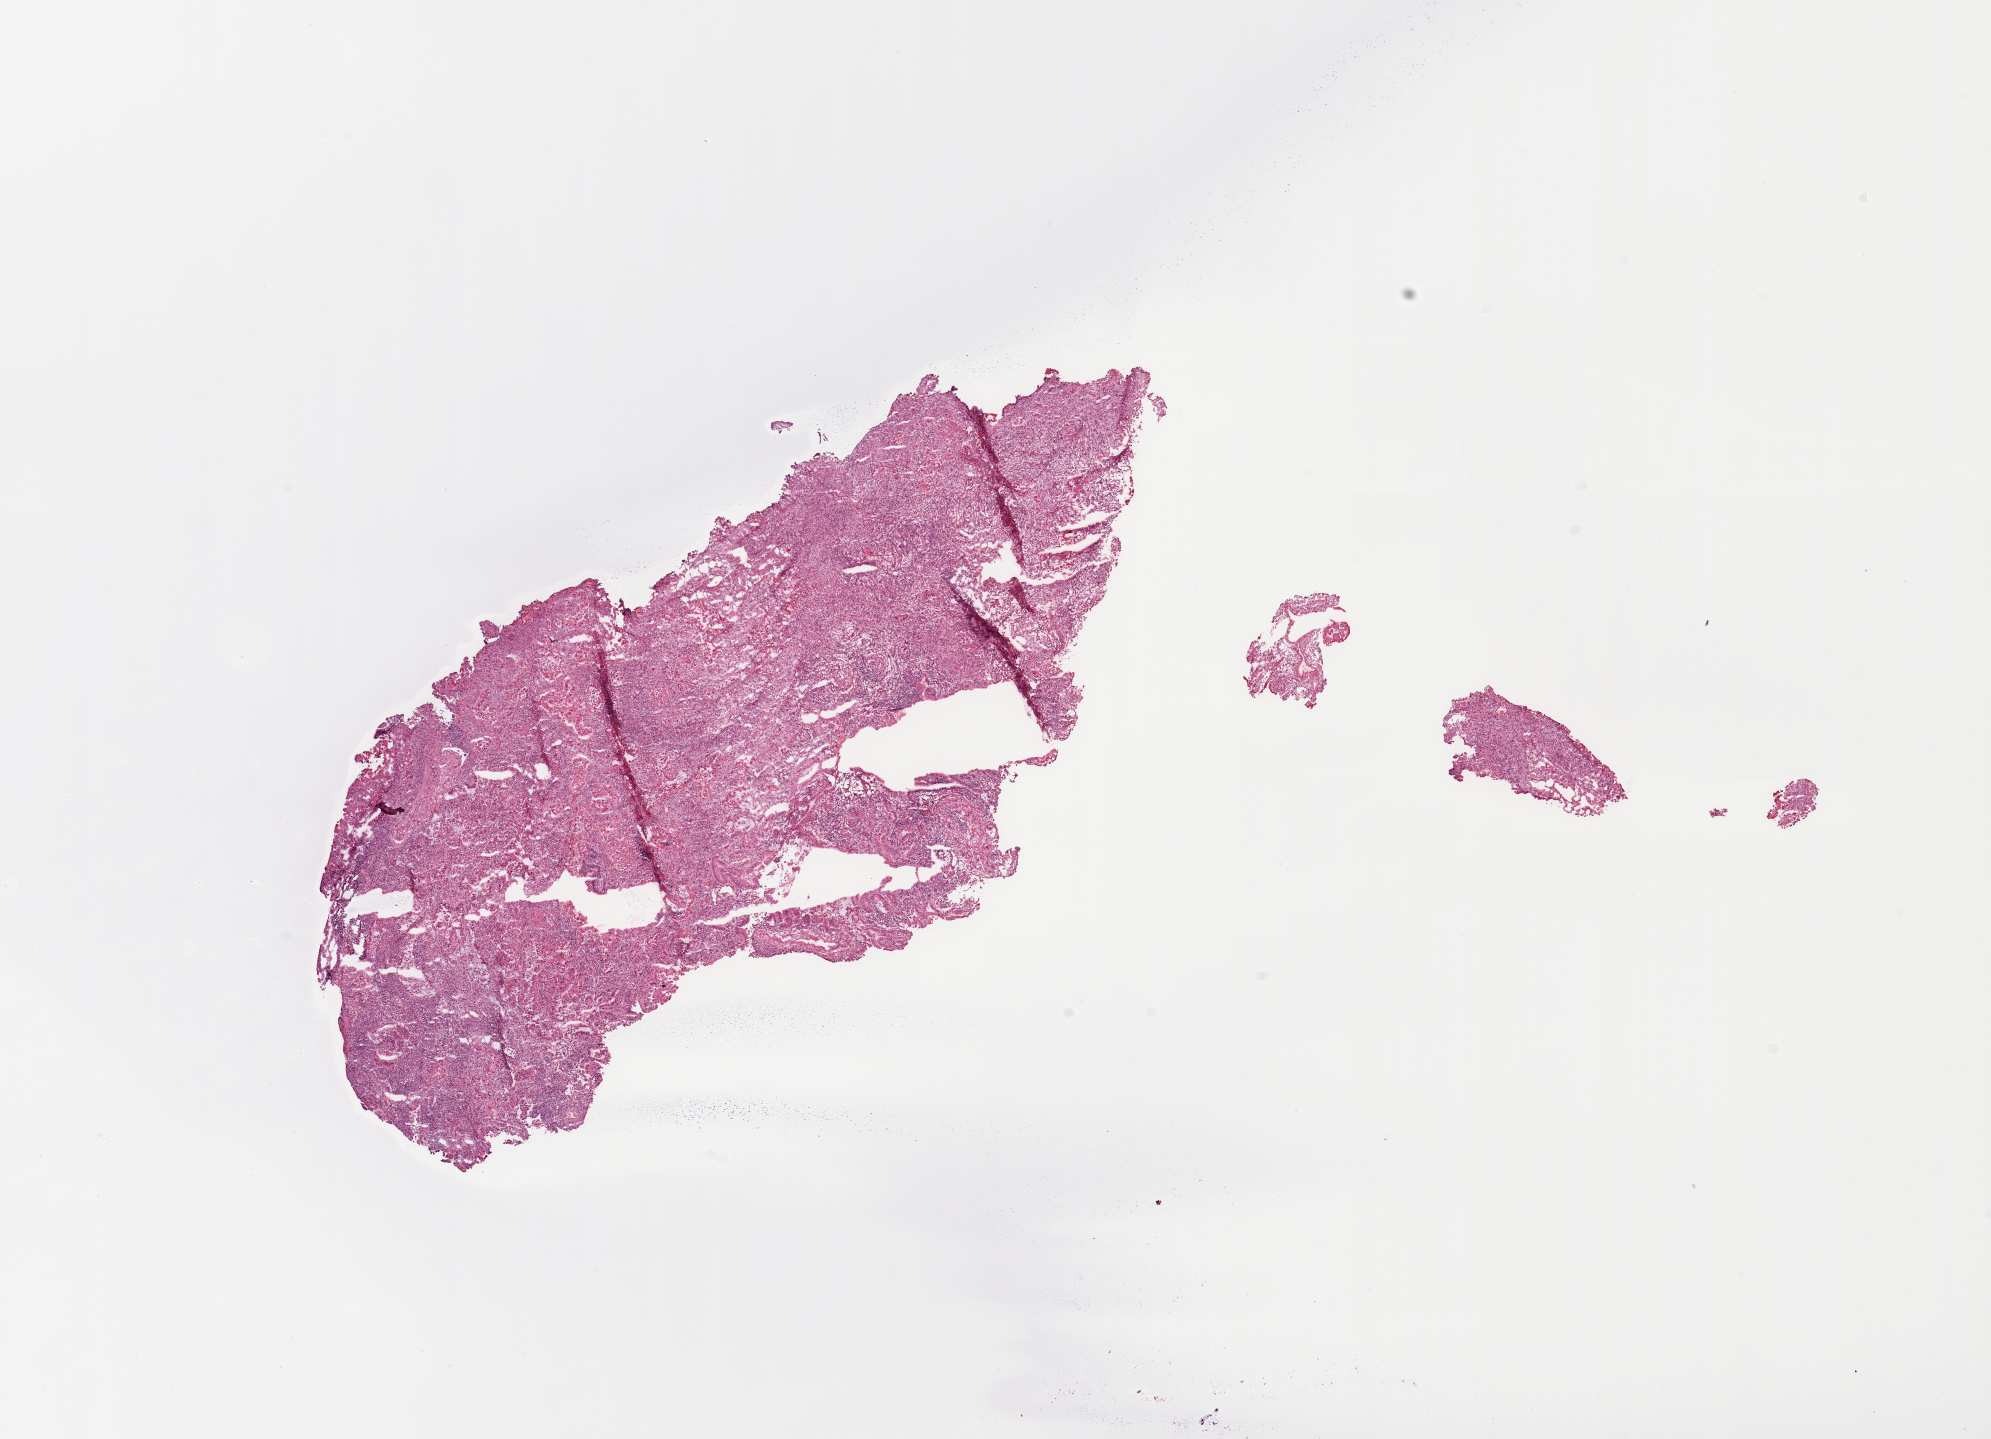
Whole-slide histology image, Hematoxylin and eosin (H&E) stained — whole scanned area (about 15.8 x 11.4 mm) shown as a low-resolution overview. Tumour tissue sample, lung. 79-year-old male patient. Histologic grade: G2 (moderately differentiated).
* primary tumour site (as recorded): right lower lobe
* diagnosis: Adenocarcinoma, NOS
* AJCC pathologic stage: IIA